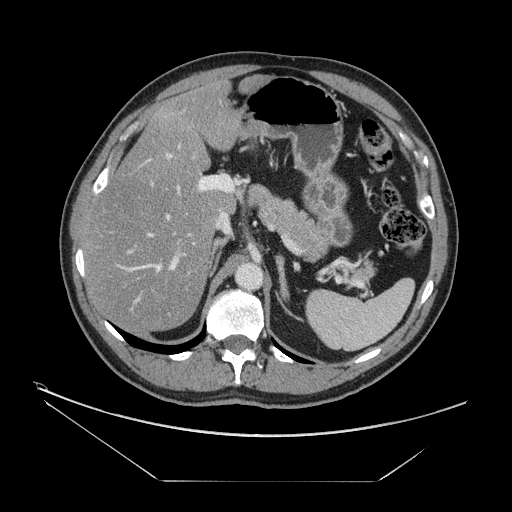
Contrast-enhanced abdominal CT, one axial slice. Position 92 of 161 along the scan axis. 120 kVp. Intravenous contrast given. Soft-tissue window (W 400 / L 40 HU). 2.5 mm slice thickness. 512 × 512 image matrix, field of view 440 × 440 mm. Male patient, age 65 years. Case-level facts recorded for this patient, not image findings: diagnosis: colorectal cancer liver metastases, imaged before liver resection; multiple liver metastases: yes; largest metastasis: 4.2 cm; disease in both lobes: yes.
Structures marked on this image (manually delineated by an expert):
- hepatic veins: bounding box [x1, y1, x2, y2] px = [117, 181, 180, 303]
- liver: [85, 84, 266, 330]
- planned liver remnant (the part of the liver to remain after resection): [85, 84, 262, 330]
- portal vein (with intrahepatic branches): [124, 152, 232, 316]